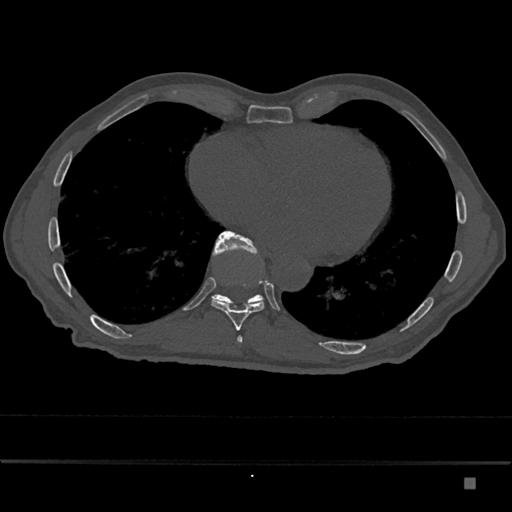
CT including the spine, one axial slice. Slice 785 of 797 in the series (ordered by position). Reconstruction kernel Br40s/3. 120 kVp. Bone window (W 1800 / L 400 HU). 0.5 mm slice thickness. 512 × 512 image matrix, field of view 390 × 390 mm. Male patient, age 72 years. Case-level facts recorded for this patient, not image findings: primary cancer: prostate.
Structures marked on this image (semi-automatically segmented with operator editing):
- T10 vertebra: bounding box (x1, y1, x2, y2) in pixels: (211, 231, 264, 307)
- T9 vertebra: (210, 235, 265, 330)